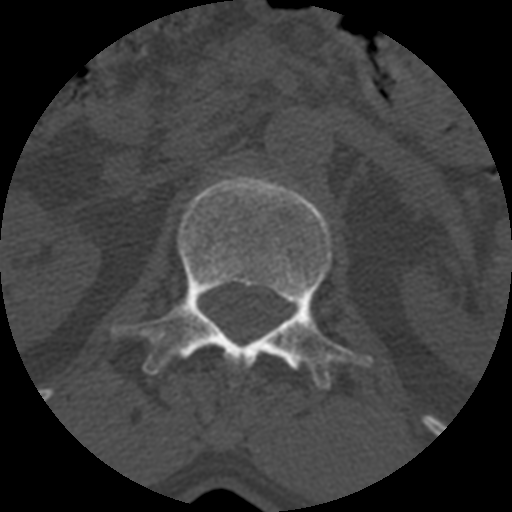
CT including the spine, one axial slice; position 360 of 399 along the scan axis; reconstruction kernel STANDARD; 120 kVp; bone window (W 1800 / L 400 HU); 512 × 512 image matrix. Patient age 71 years. Case-level facts recorded for this patient, not image findings: primary cancer: prostate.
Annotated regions visible in this slice (semi-automatic segmentation, software-assisted and operator-edited):
- L1 vertebra: bounding box <113,178,372,389> (left, top, right, bottom; pixels)